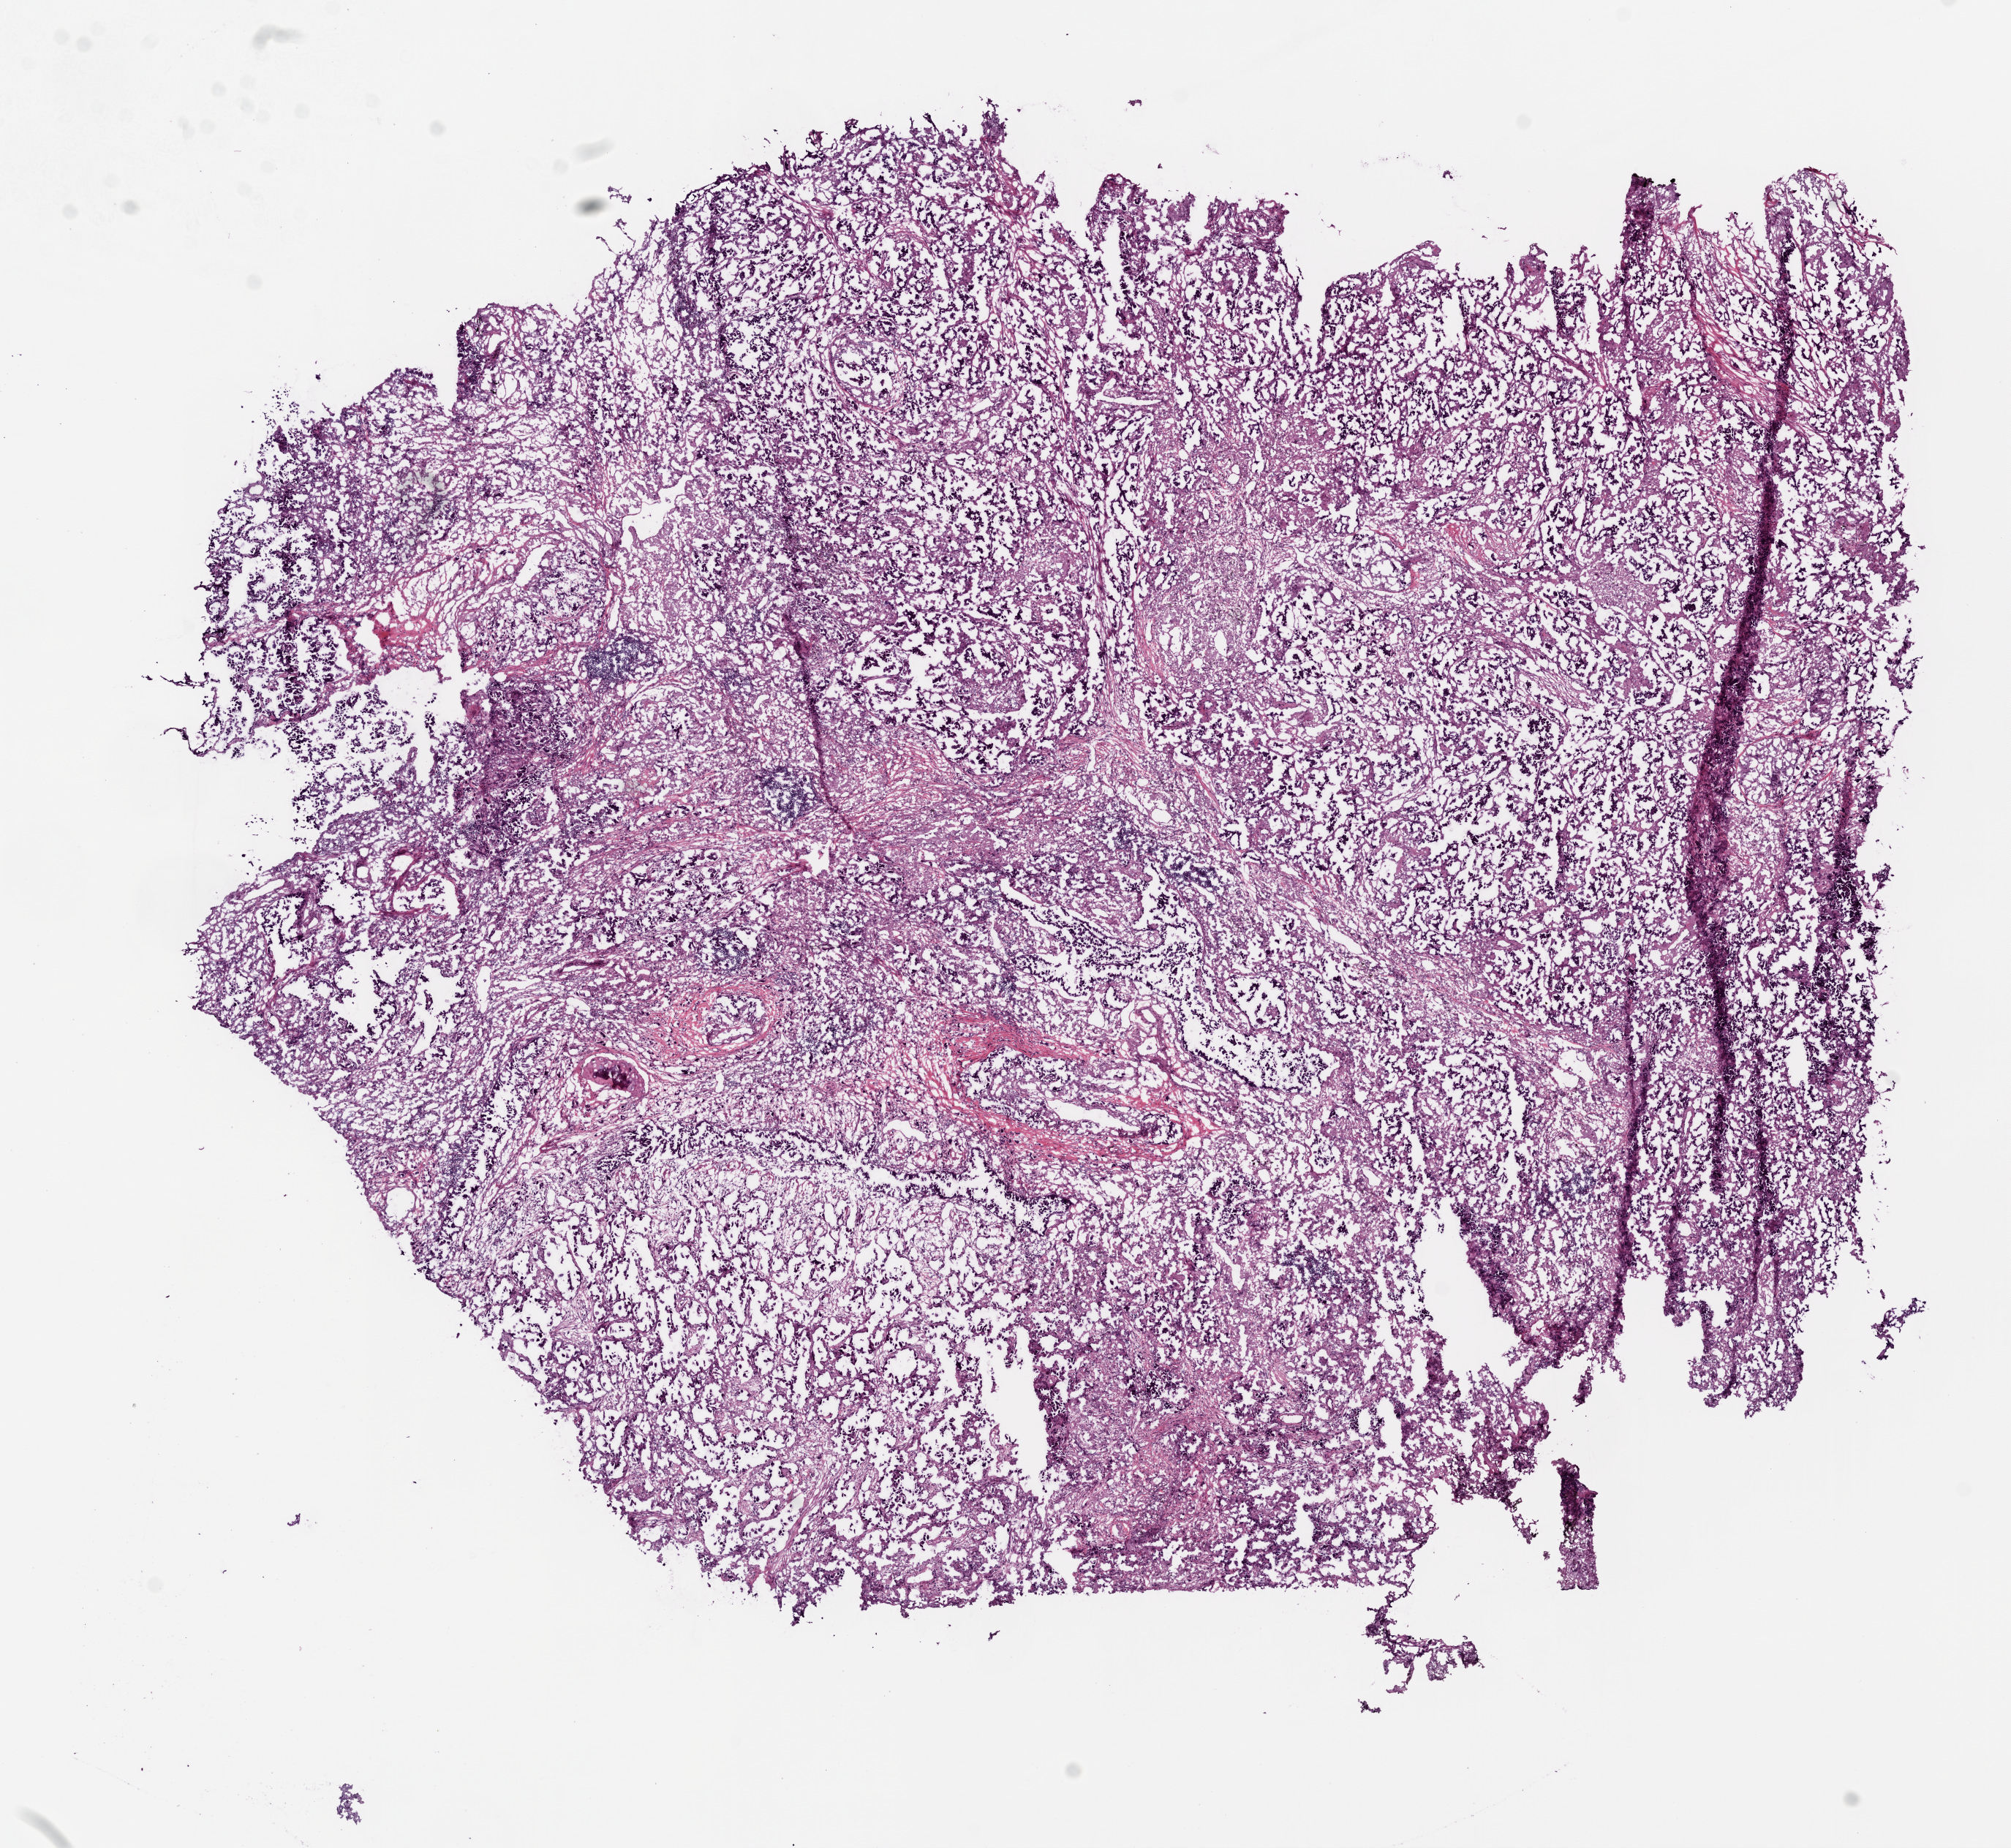
Whole-slide histology image, Hematoxylin and eosin (H&E) stained, low-resolution overview of the scanned area, about 11.0 x 10.1 mm; frozen section from the bottom of the tissue portion; primary tumour sample from the lung. Female, age 69 years at initial diagnosis. Slide review estimates, as recorded: tumour cells 85%, tumour nuclei 70%.
Pathologic diagnosis: Adenocarcinoma, NOS.